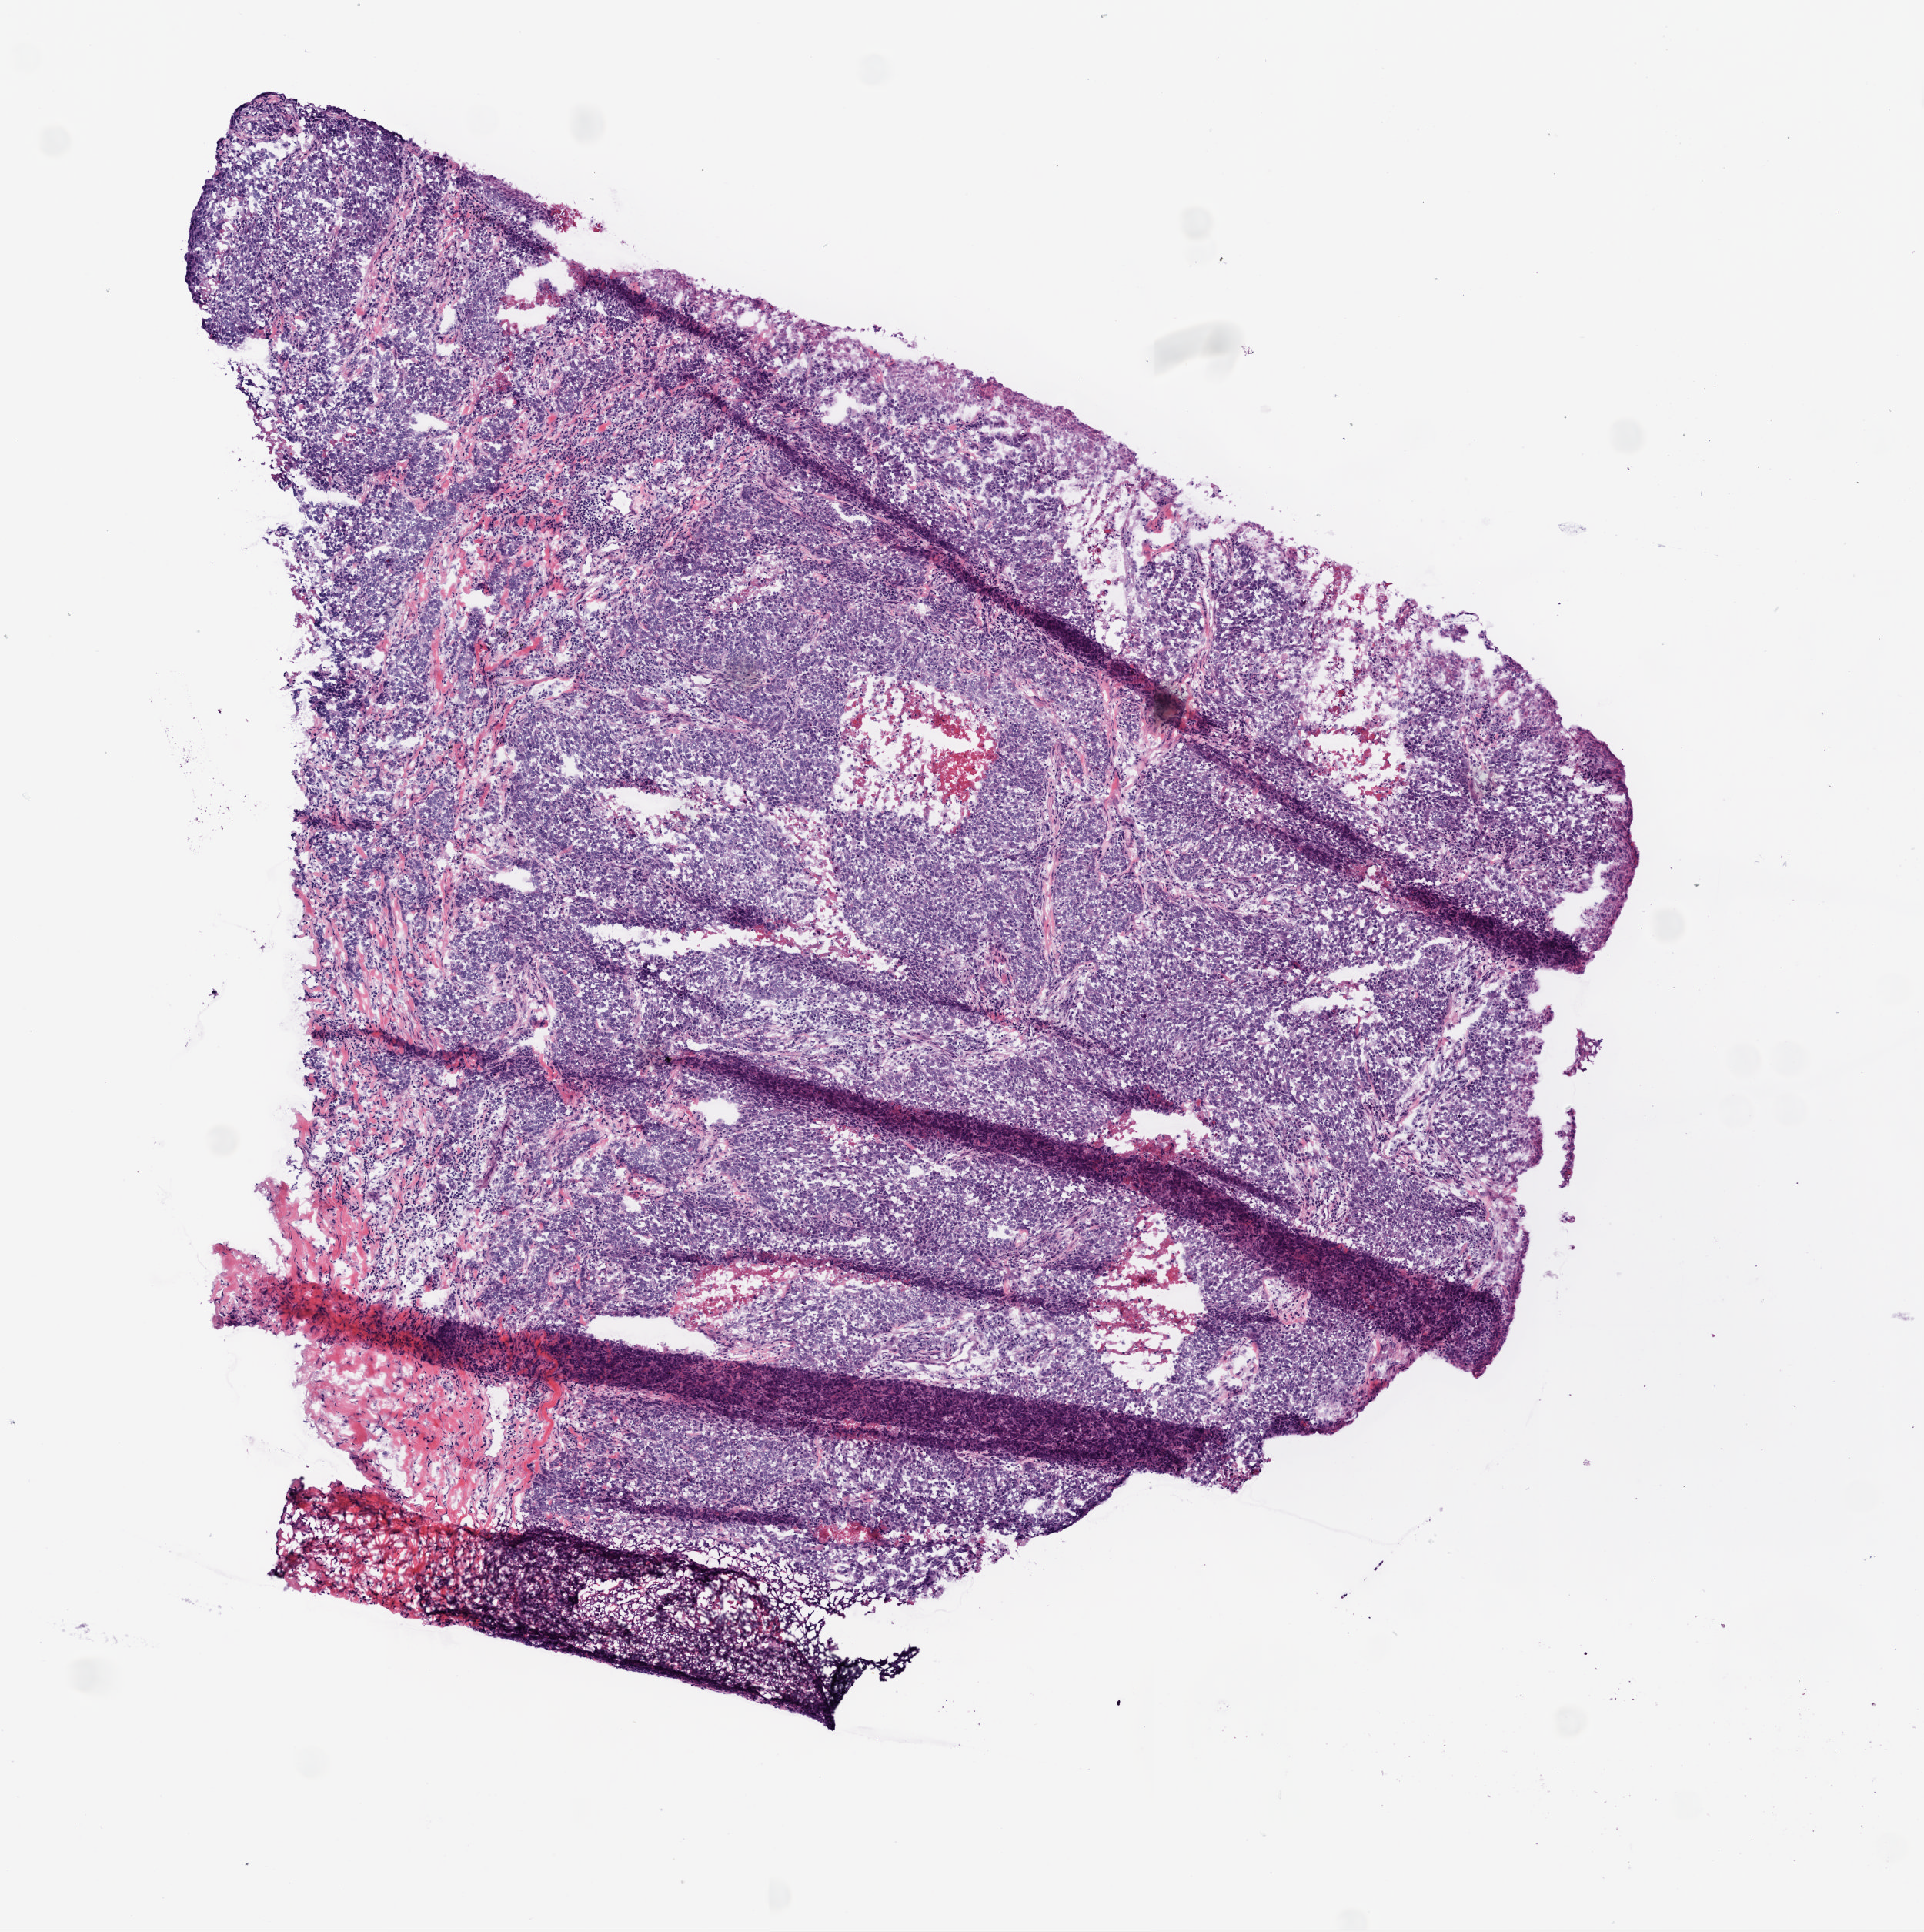
Whole-slide histology image, H&E-stained — low-resolution overview of the scanned area, about 5.0 x 5.0 mm. Frozen section from the bottom of the tissue portion. Primary tumour sample from the lung. Male, age 81 years at initial diagnosis. Pathologist review of this section (percent, as recorded): tumour cells 90%, tumour nuclei 90%, normal cells 0%, stromal cells 5%, necrosis 5%. Inflammatory infiltration, as recorded: lymphocyte infiltration 5%.
AJCC pathologic stage: IIB. Pathologic diagnosis: Squamous cell carcinoma, NOS (lower lobe, lung).